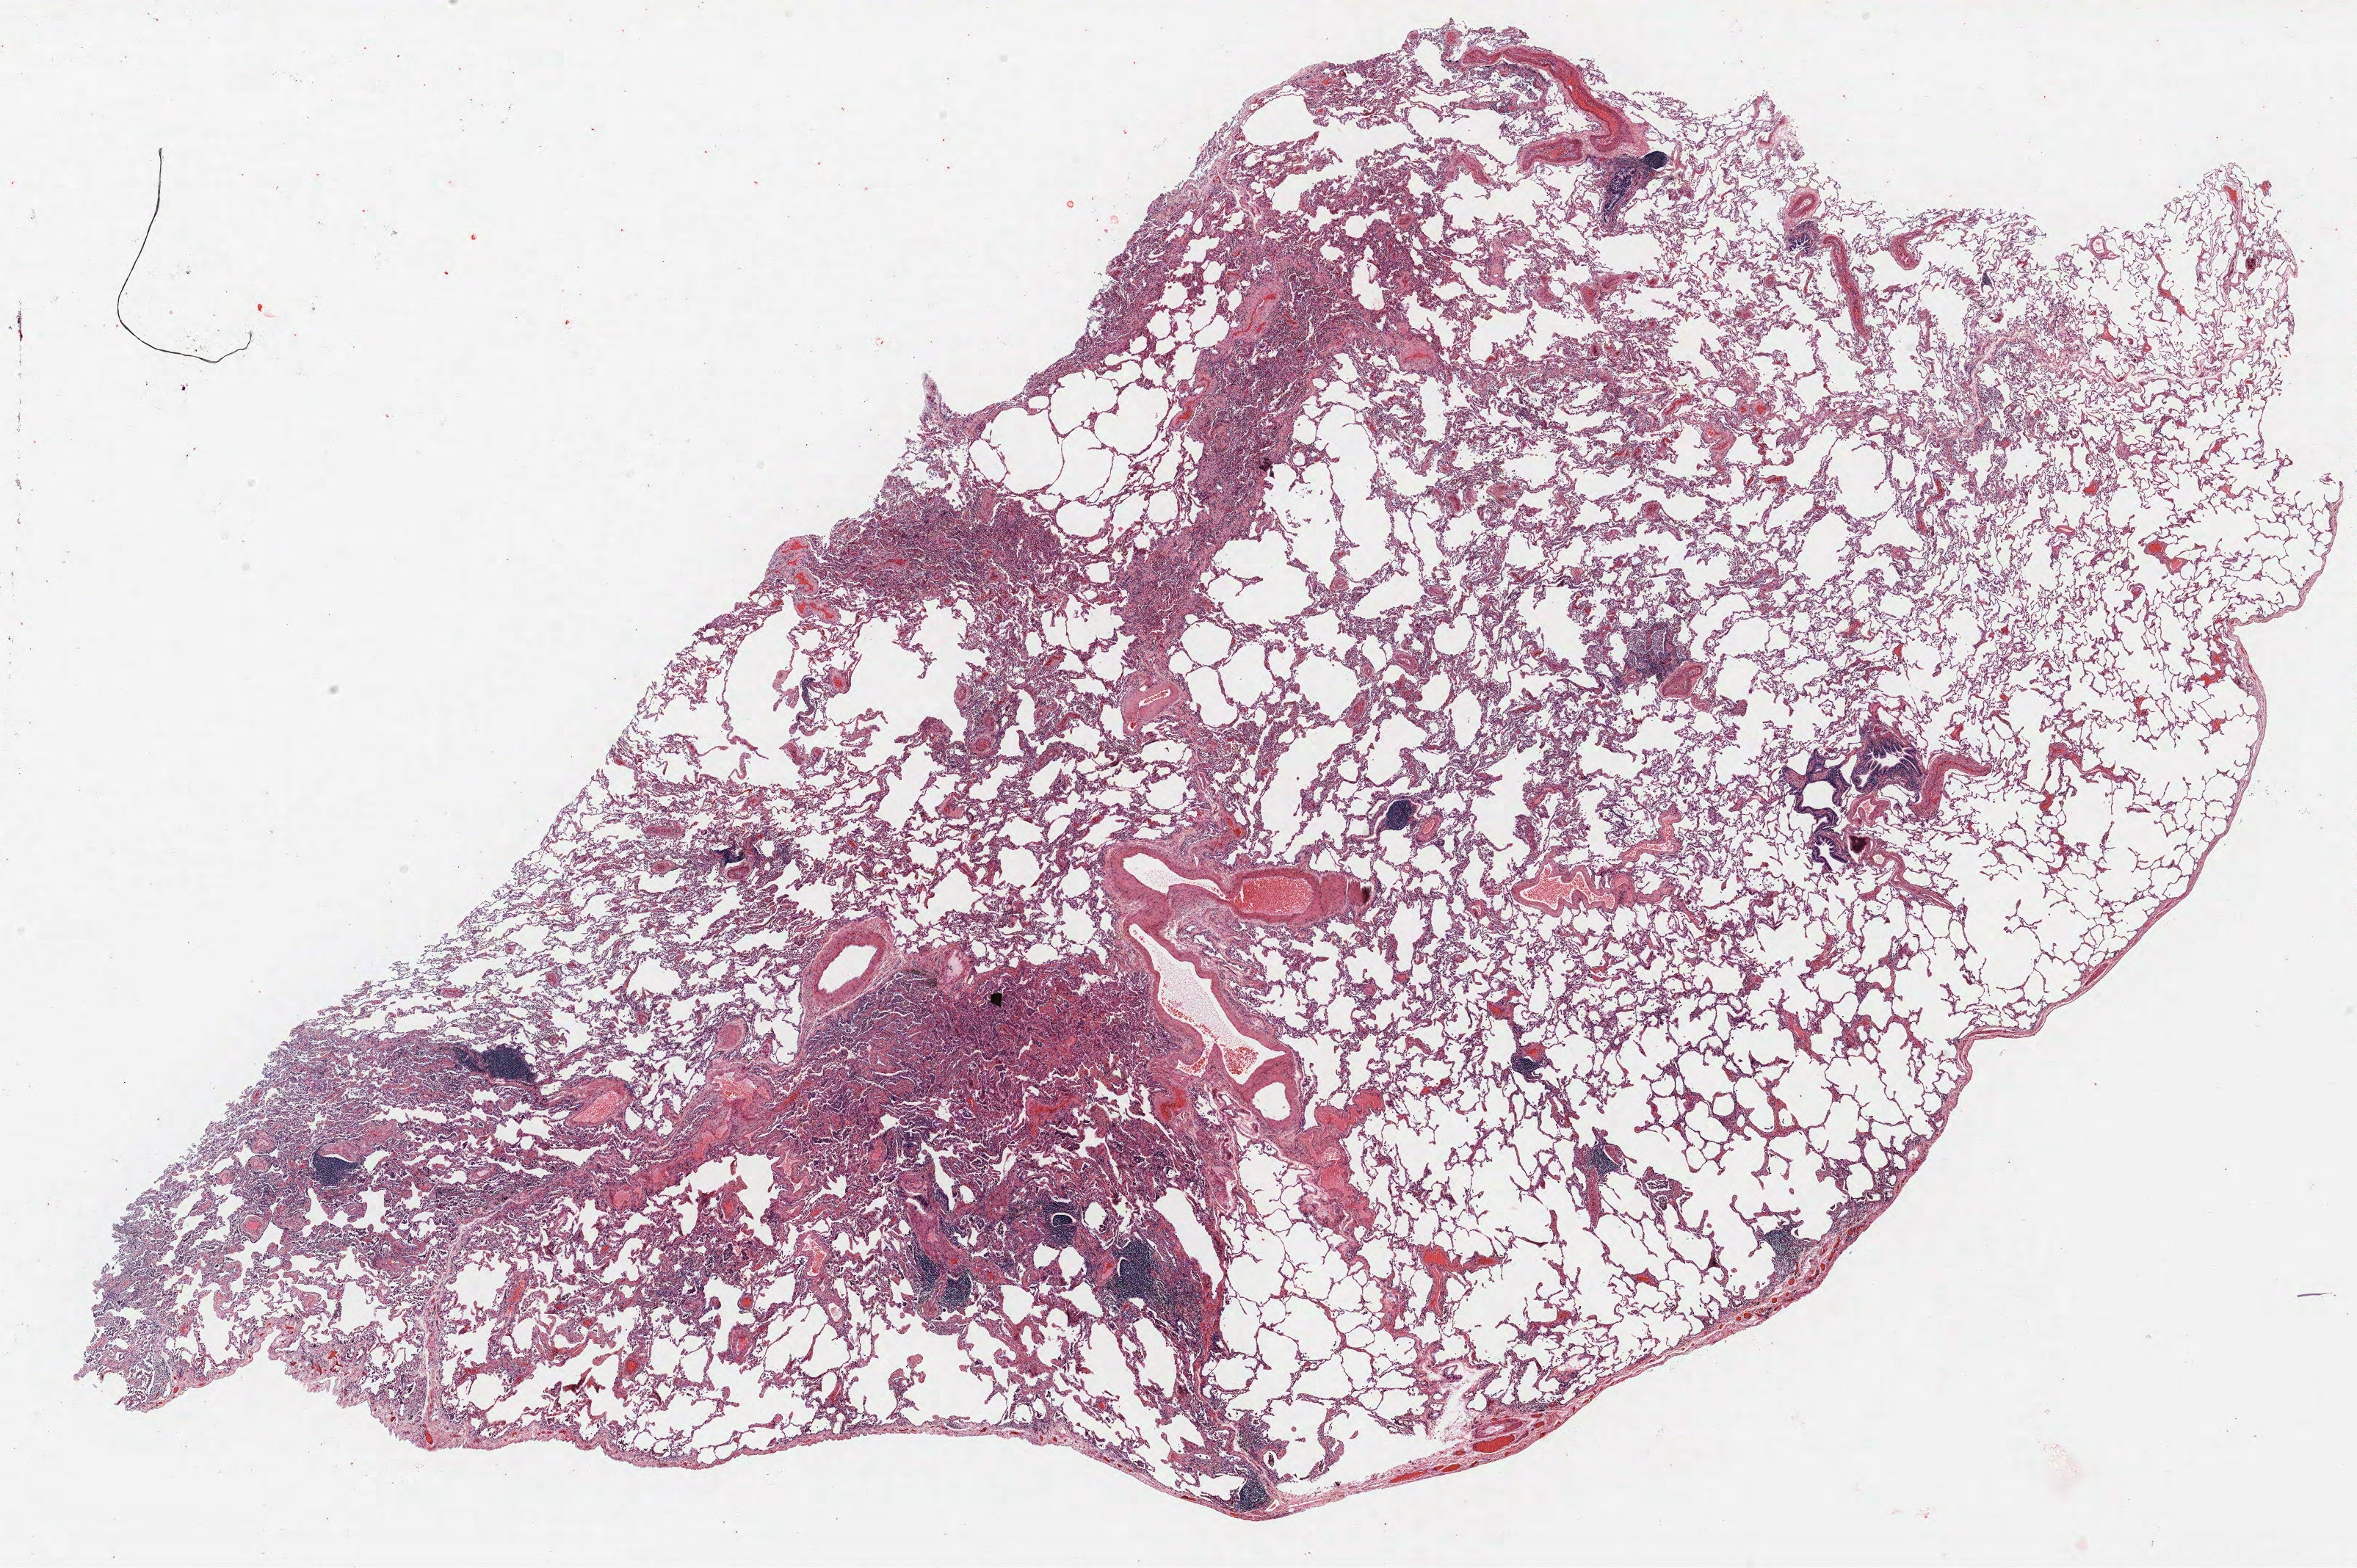
Hematoxylin and eosin (H&E) stained whole-slide image — a low-resolution overview of the entire scanned area, about 25.7 x 17.1 mm, FFPE section, lung tissue. Female patient, aged 64 at enrolment. Current smoker at enrolment. Grade: moderately differentiated (G2).
Tumour size (pathology): 15 mm. Primary tumour location (clinical record): left upper lobe. Stage (AJCC 6th edition): IA. Participant's lung-cancer diagnosis: Squamous cell carcinoma, NOS.